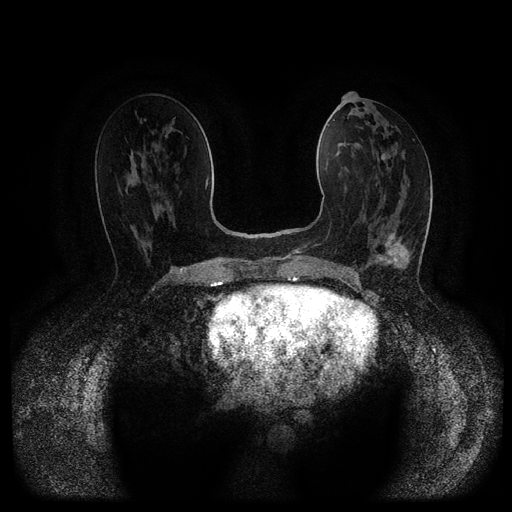
Breast MRI (dynamic contrast-enhanced, multi-phase), one axial slice. Position 50 of 116 along the scan axis. Dynamic contrast-enhanced series, time point 2 of 5 at this slice position (early post-contrast). 1.5 T. TE 2.6 ms, TR 5.4 ms. 2 mm slice thickness. 512 × 512 image matrix, field of view 340 × 340 mm. Patient: female, 61 years.
Structures marked on this image (semi-automatic segmentation, software-assisted and operator-edited):
- breast lesion (labelled 'tumour' in the annotation; benign lesions carry a separate 'benign' label): bounding box [x1, y1, x2, y2] px = [375, 232, 396, 266]